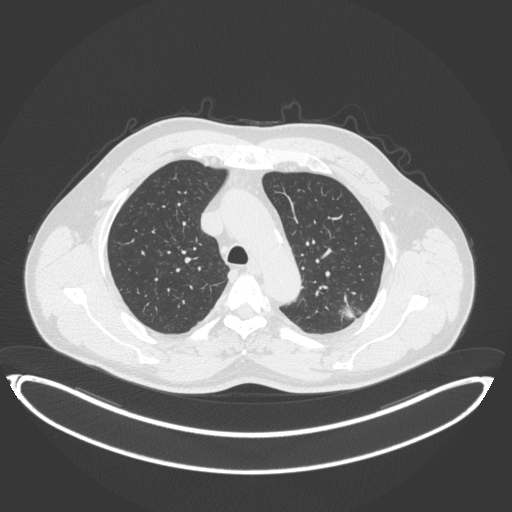
Chest CT, one axial slice; slice 269 of 399 in the series (ordered by position); reconstruction kernel B31f; lung window (W 1500 / L -600 HU); 1 mm slice thickness; 512 × 512 image matrix, field of view 469 × 469 mm. Patient: male, 58 years. Case-level facts recorded for this patient, not image findings: clinical TNM (as recorded): T1c N0 M0; histopathological grade: G1-2.
Structures marked on this image (rectangle marked by the reading radiologist):
- lung tumour (recorded histology: adenocarcinoma): bounding box (x1, y1, x2, y2) in pixels: (337, 300, 364, 325)